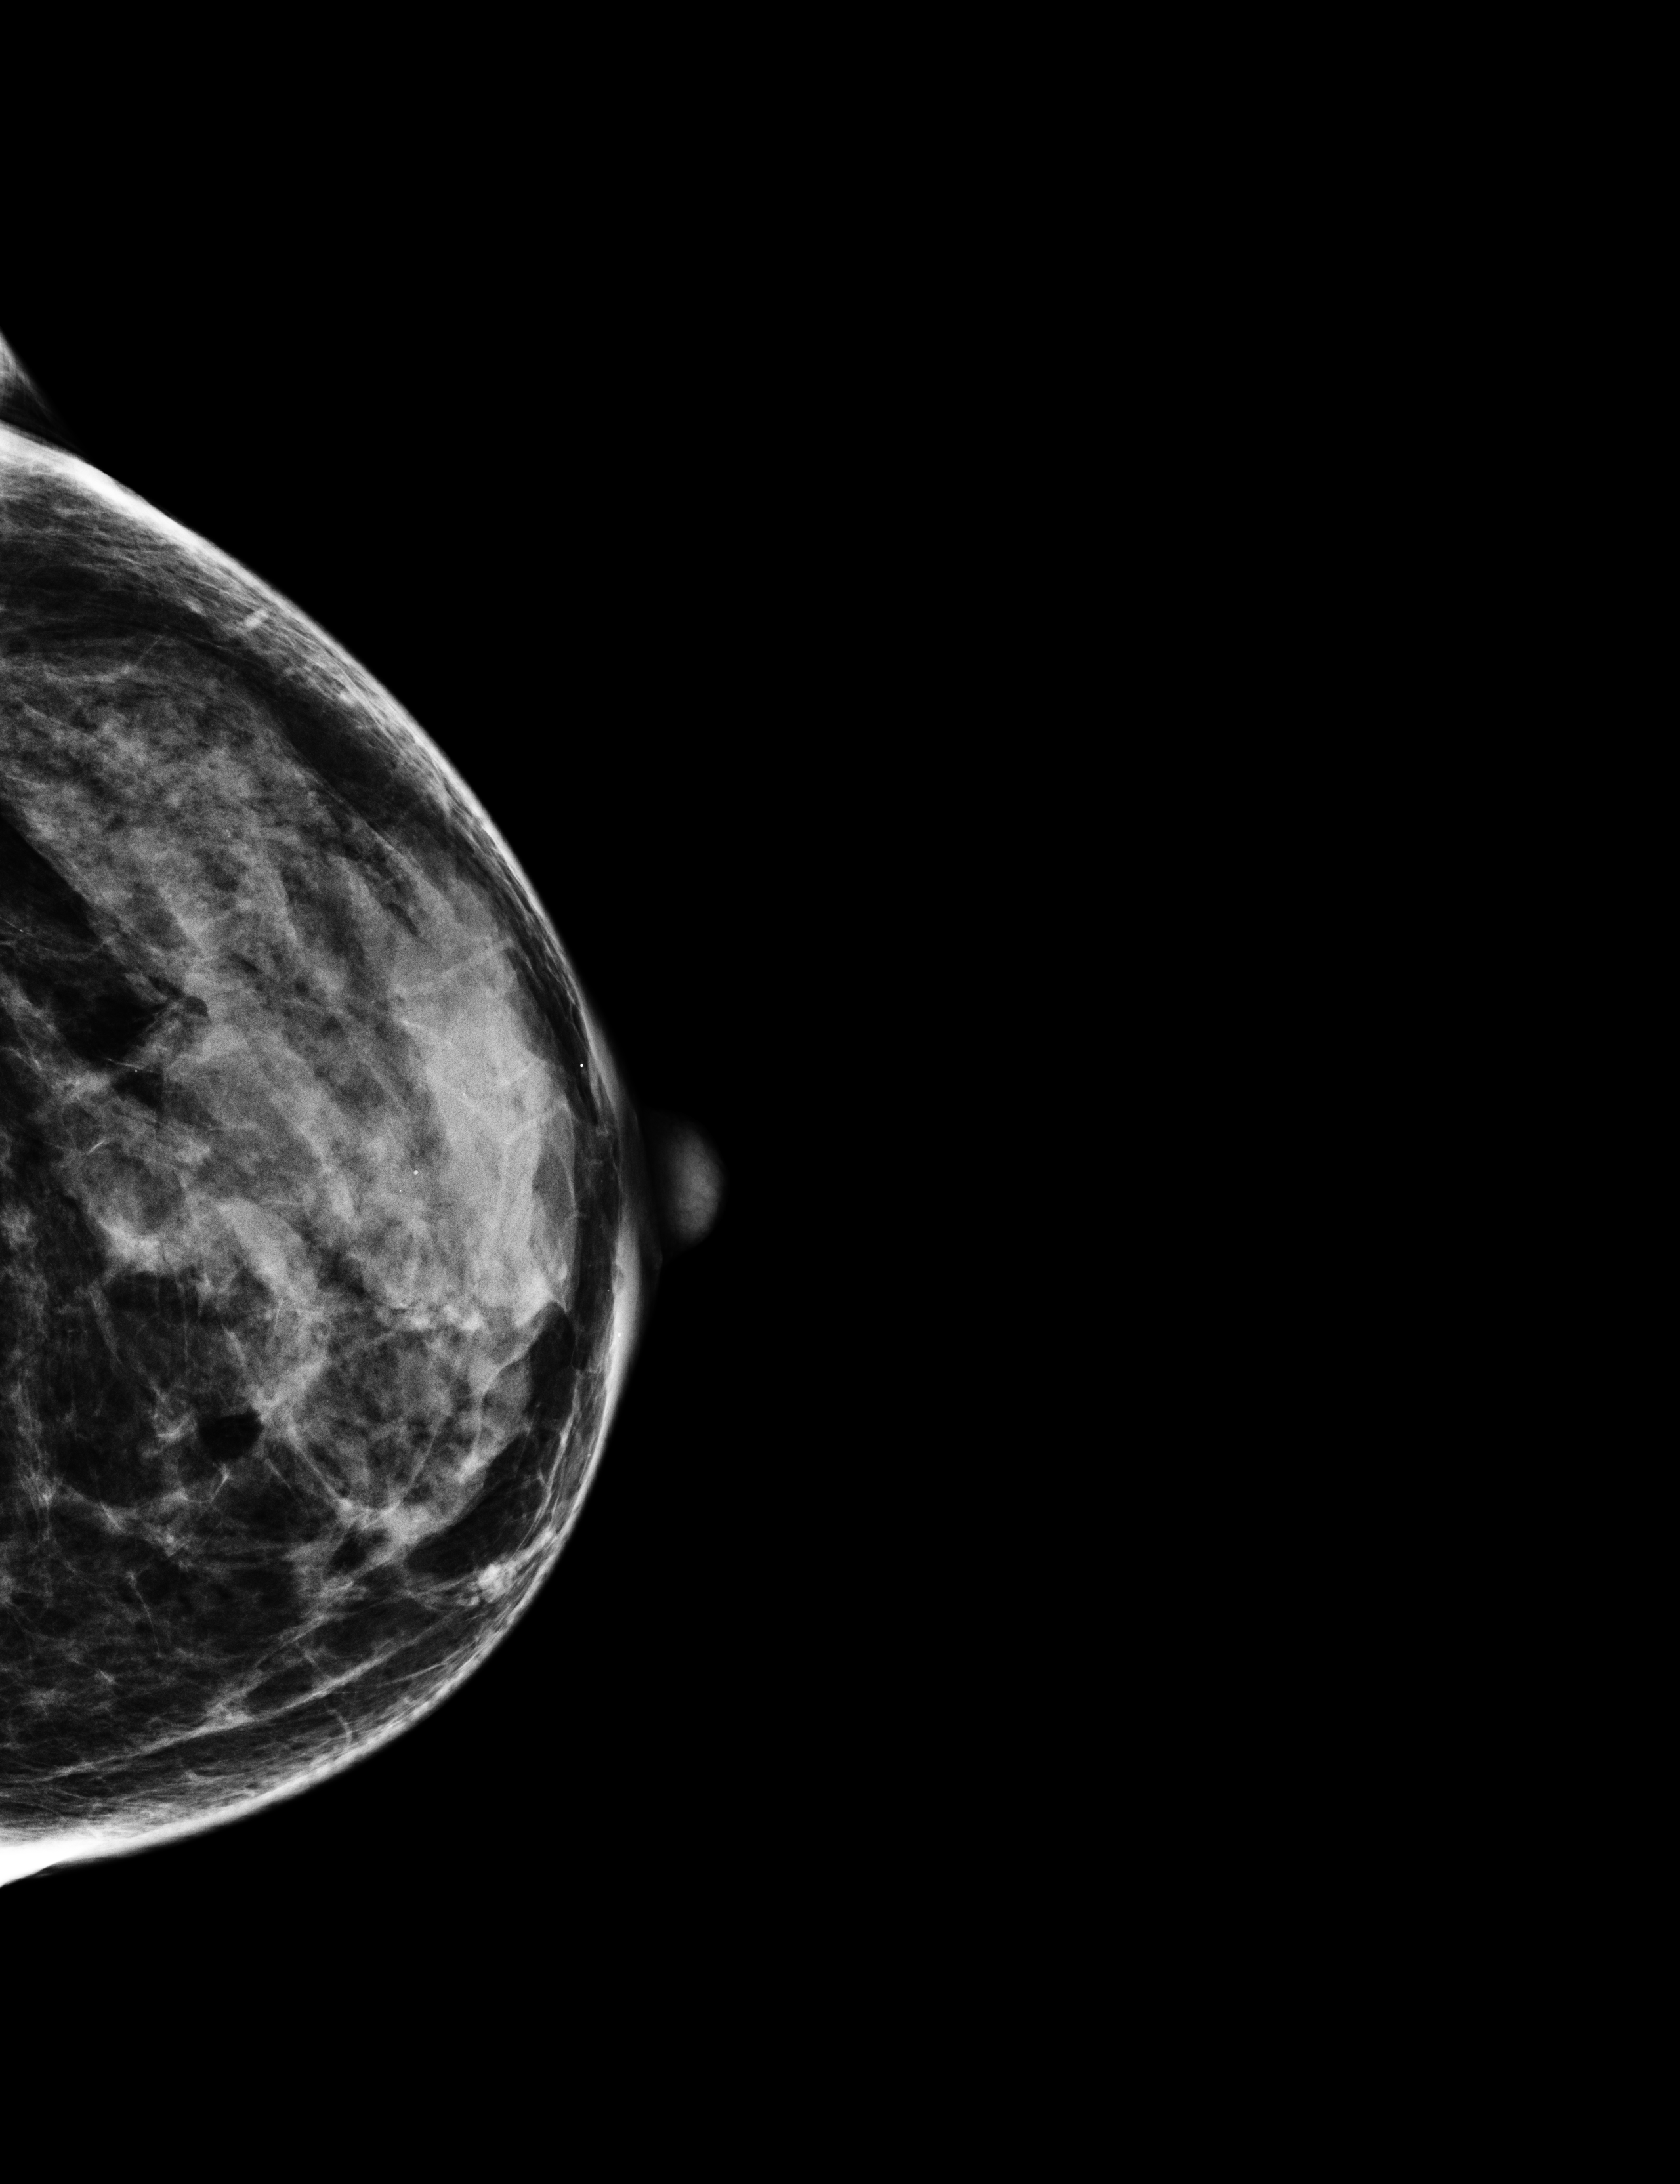
Annual screening mammography examination; compressed breast thickness 44 mm. Patient: female, 57 years.
Image type: full-field digital mammogram. Breast: left. Projection: cranio-caudal projection.